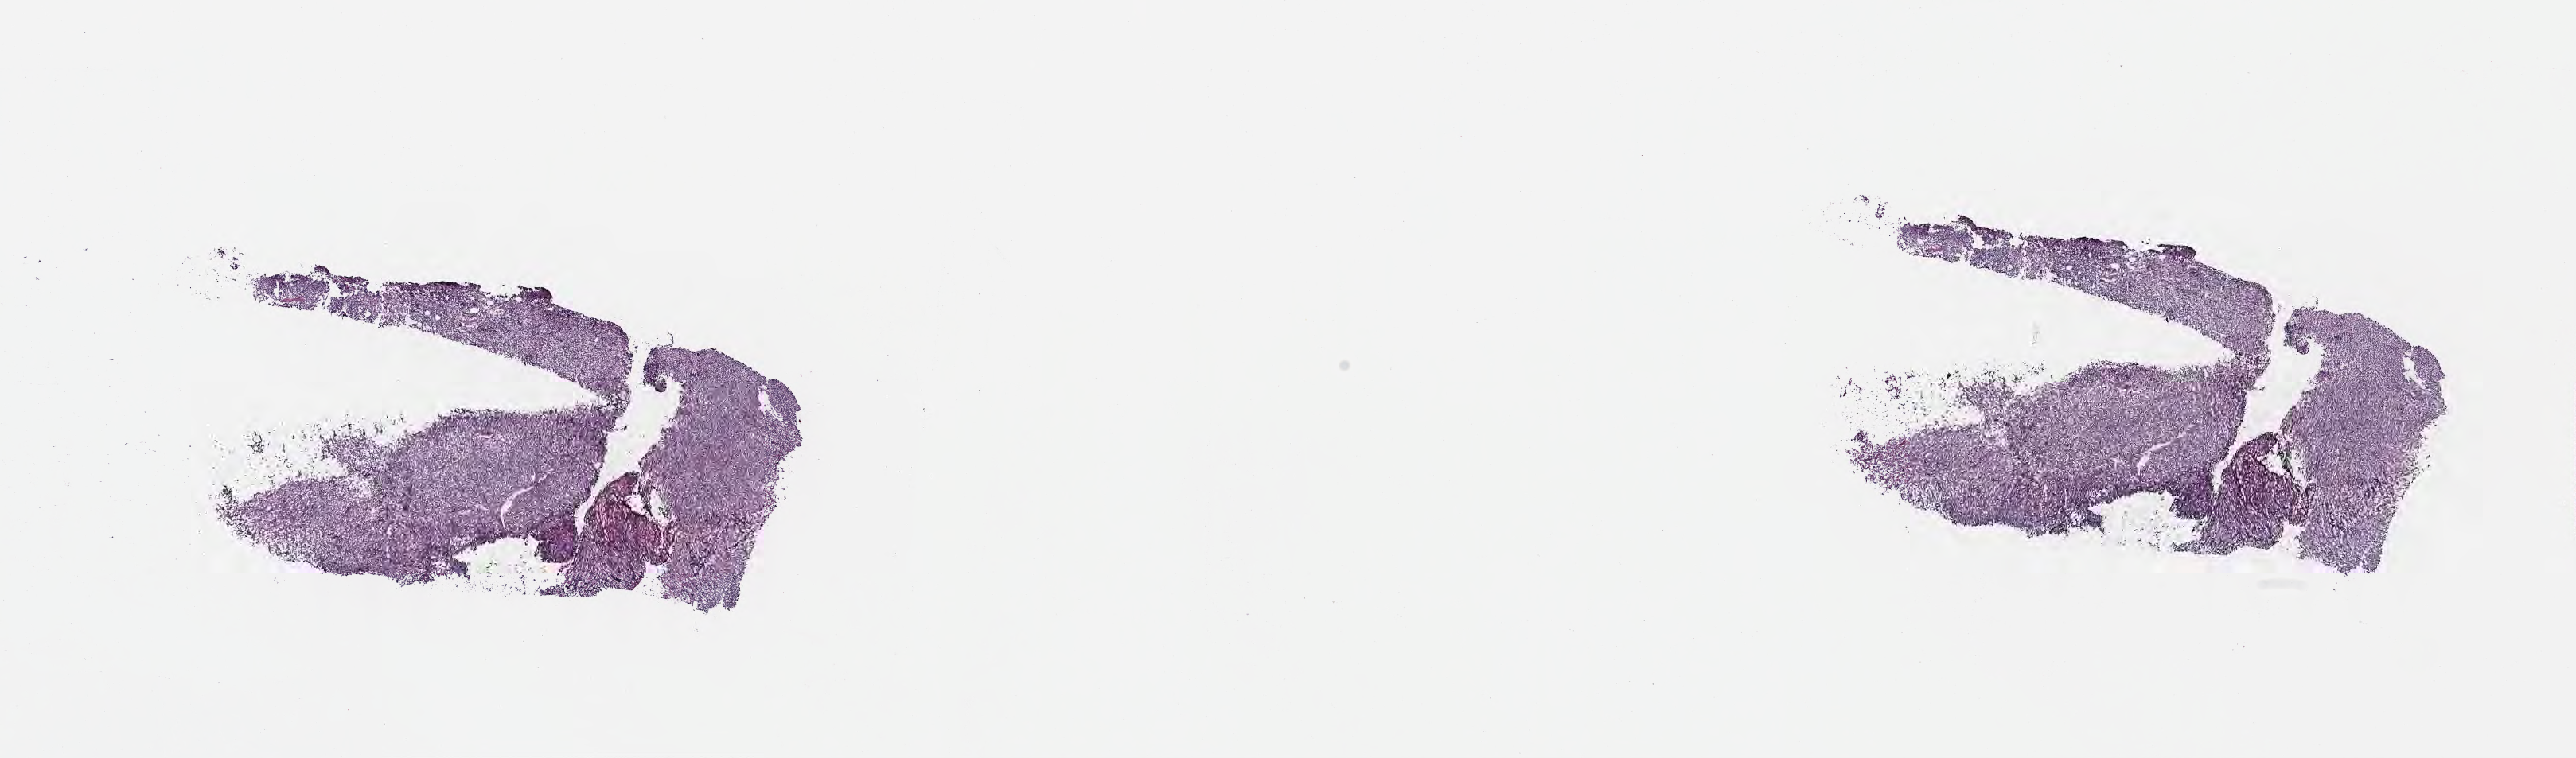
H&E whole-slide image — low-resolution overview of the scanned area, about 26.2 x 7.7 mm; frozen section; primary tumor; anatomic site: lymph node of head and neck. Male patient; age at initial diagnosis 5 years. Pathologist review of this section (percent, as recorded): tumor cells 90%, tumor nuclei 95%.
Diagnosis: Burkitt lymphoma, NOS.